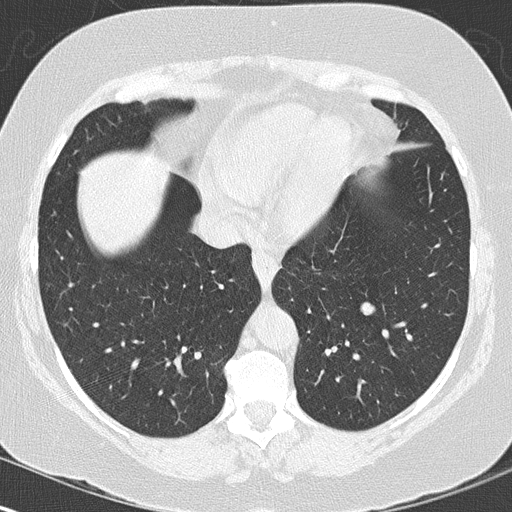
Low-dose screening chest CT, one axial slice; reconstruction kernel B50f; 120 kVp; lung window (W 1500 / L -600 HU); 2 mm slice thickness; 512 × 512 image matrix, field of view 316 × 316 mm.
Annotated regions visible in this slice (expert manual segmentation):
- lesion 1 (tumor, lower lobe of left lung): bounding box [x1, y1, x2, y2] px = [361, 302, 374, 316]